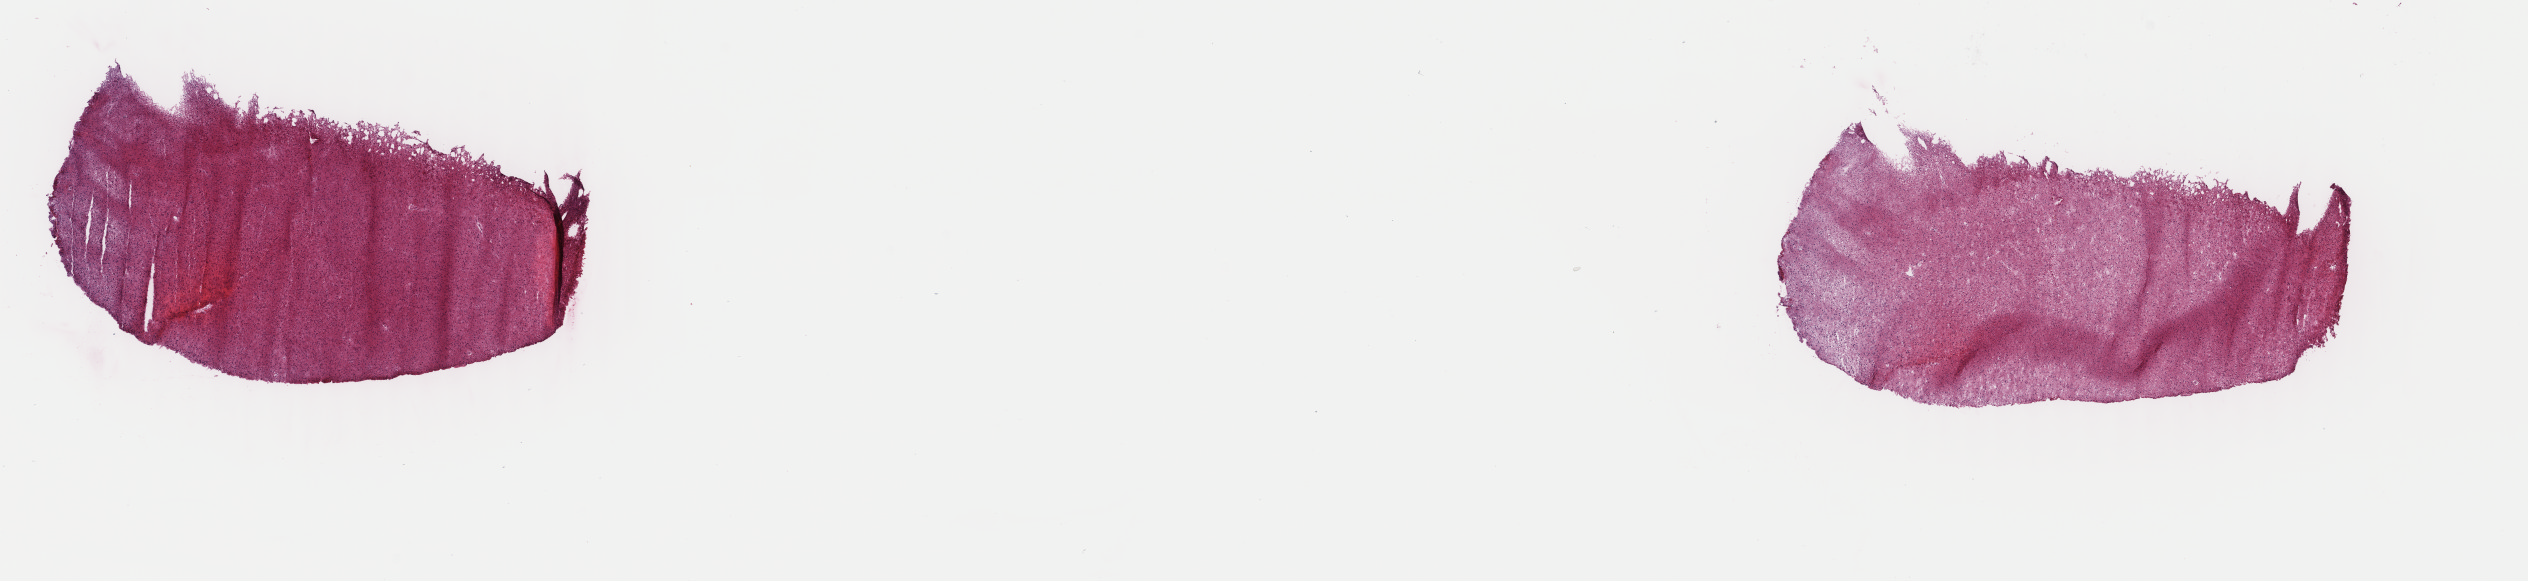
Digitized H&E tissue section (whole slide) — shown as a low-resolution overview of the whole scanned area (about 20.1 x 4.6 mm, from a 40x scan); frozen section from the top of the tissue portion; primary tumour sample from the brain. Male, age 39 years at initial diagnosis. Histologic grade: G3 (poorly differentiated). Composition of this section per pathologist review: tumour cells 70%, tumour nuclei 90%, normal cells 10%, stromal cells 20%, necrosis 0%. Infiltration values recorded for this section: lymphocyte infiltration 0%, monocyte infiltration 0%, neutrophil infiltration 0%.
- diagnosis: Mixed glioma (cerebrum)
- laterality: right